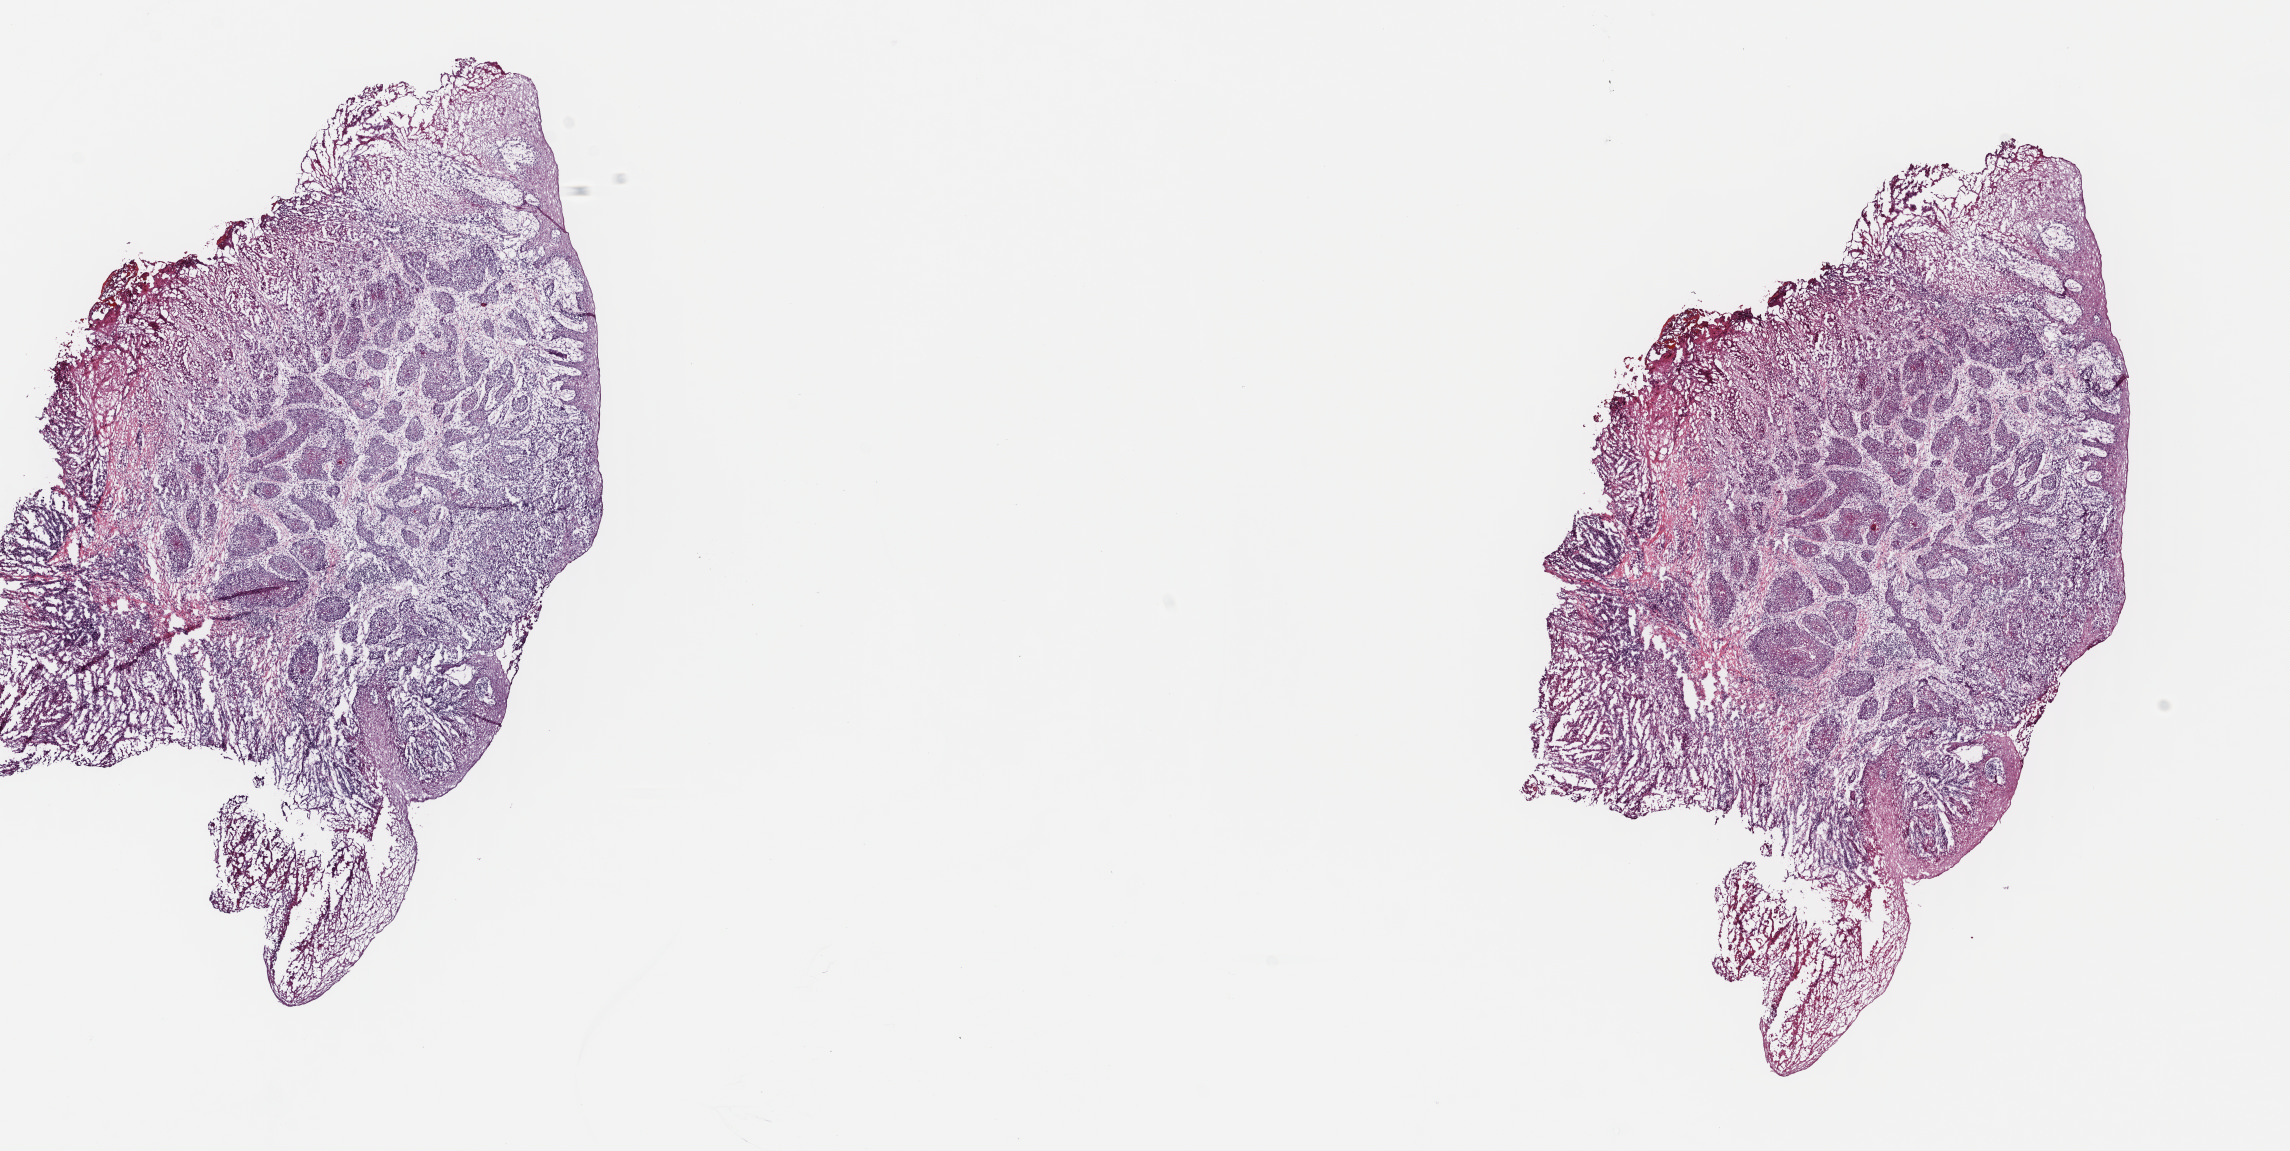
H&E-stained whole-slide image — a low-resolution overview of the entire scanned area, about 18.0 x 9.0 mm (acquisition: 40x scan). Frozen section. Head and neck, primary tumour sample. Male patient; age at initial diagnosis 59 years. Histologic grade: G2 (moderately differentiated). Composition of this section per pathologist review: tumour cells 90%, tumour nuclei 65%, normal cells 10%, stromal cells 0%, necrosis 0%. Infiltration values recorded for this section: lymphocyte infiltration 10%, monocyte infiltration 0%, neutrophil infiltration 1%.
Laterality: right. Diagnosis: Squamous cell carcinoma, NOS (oropharynx, NOS).